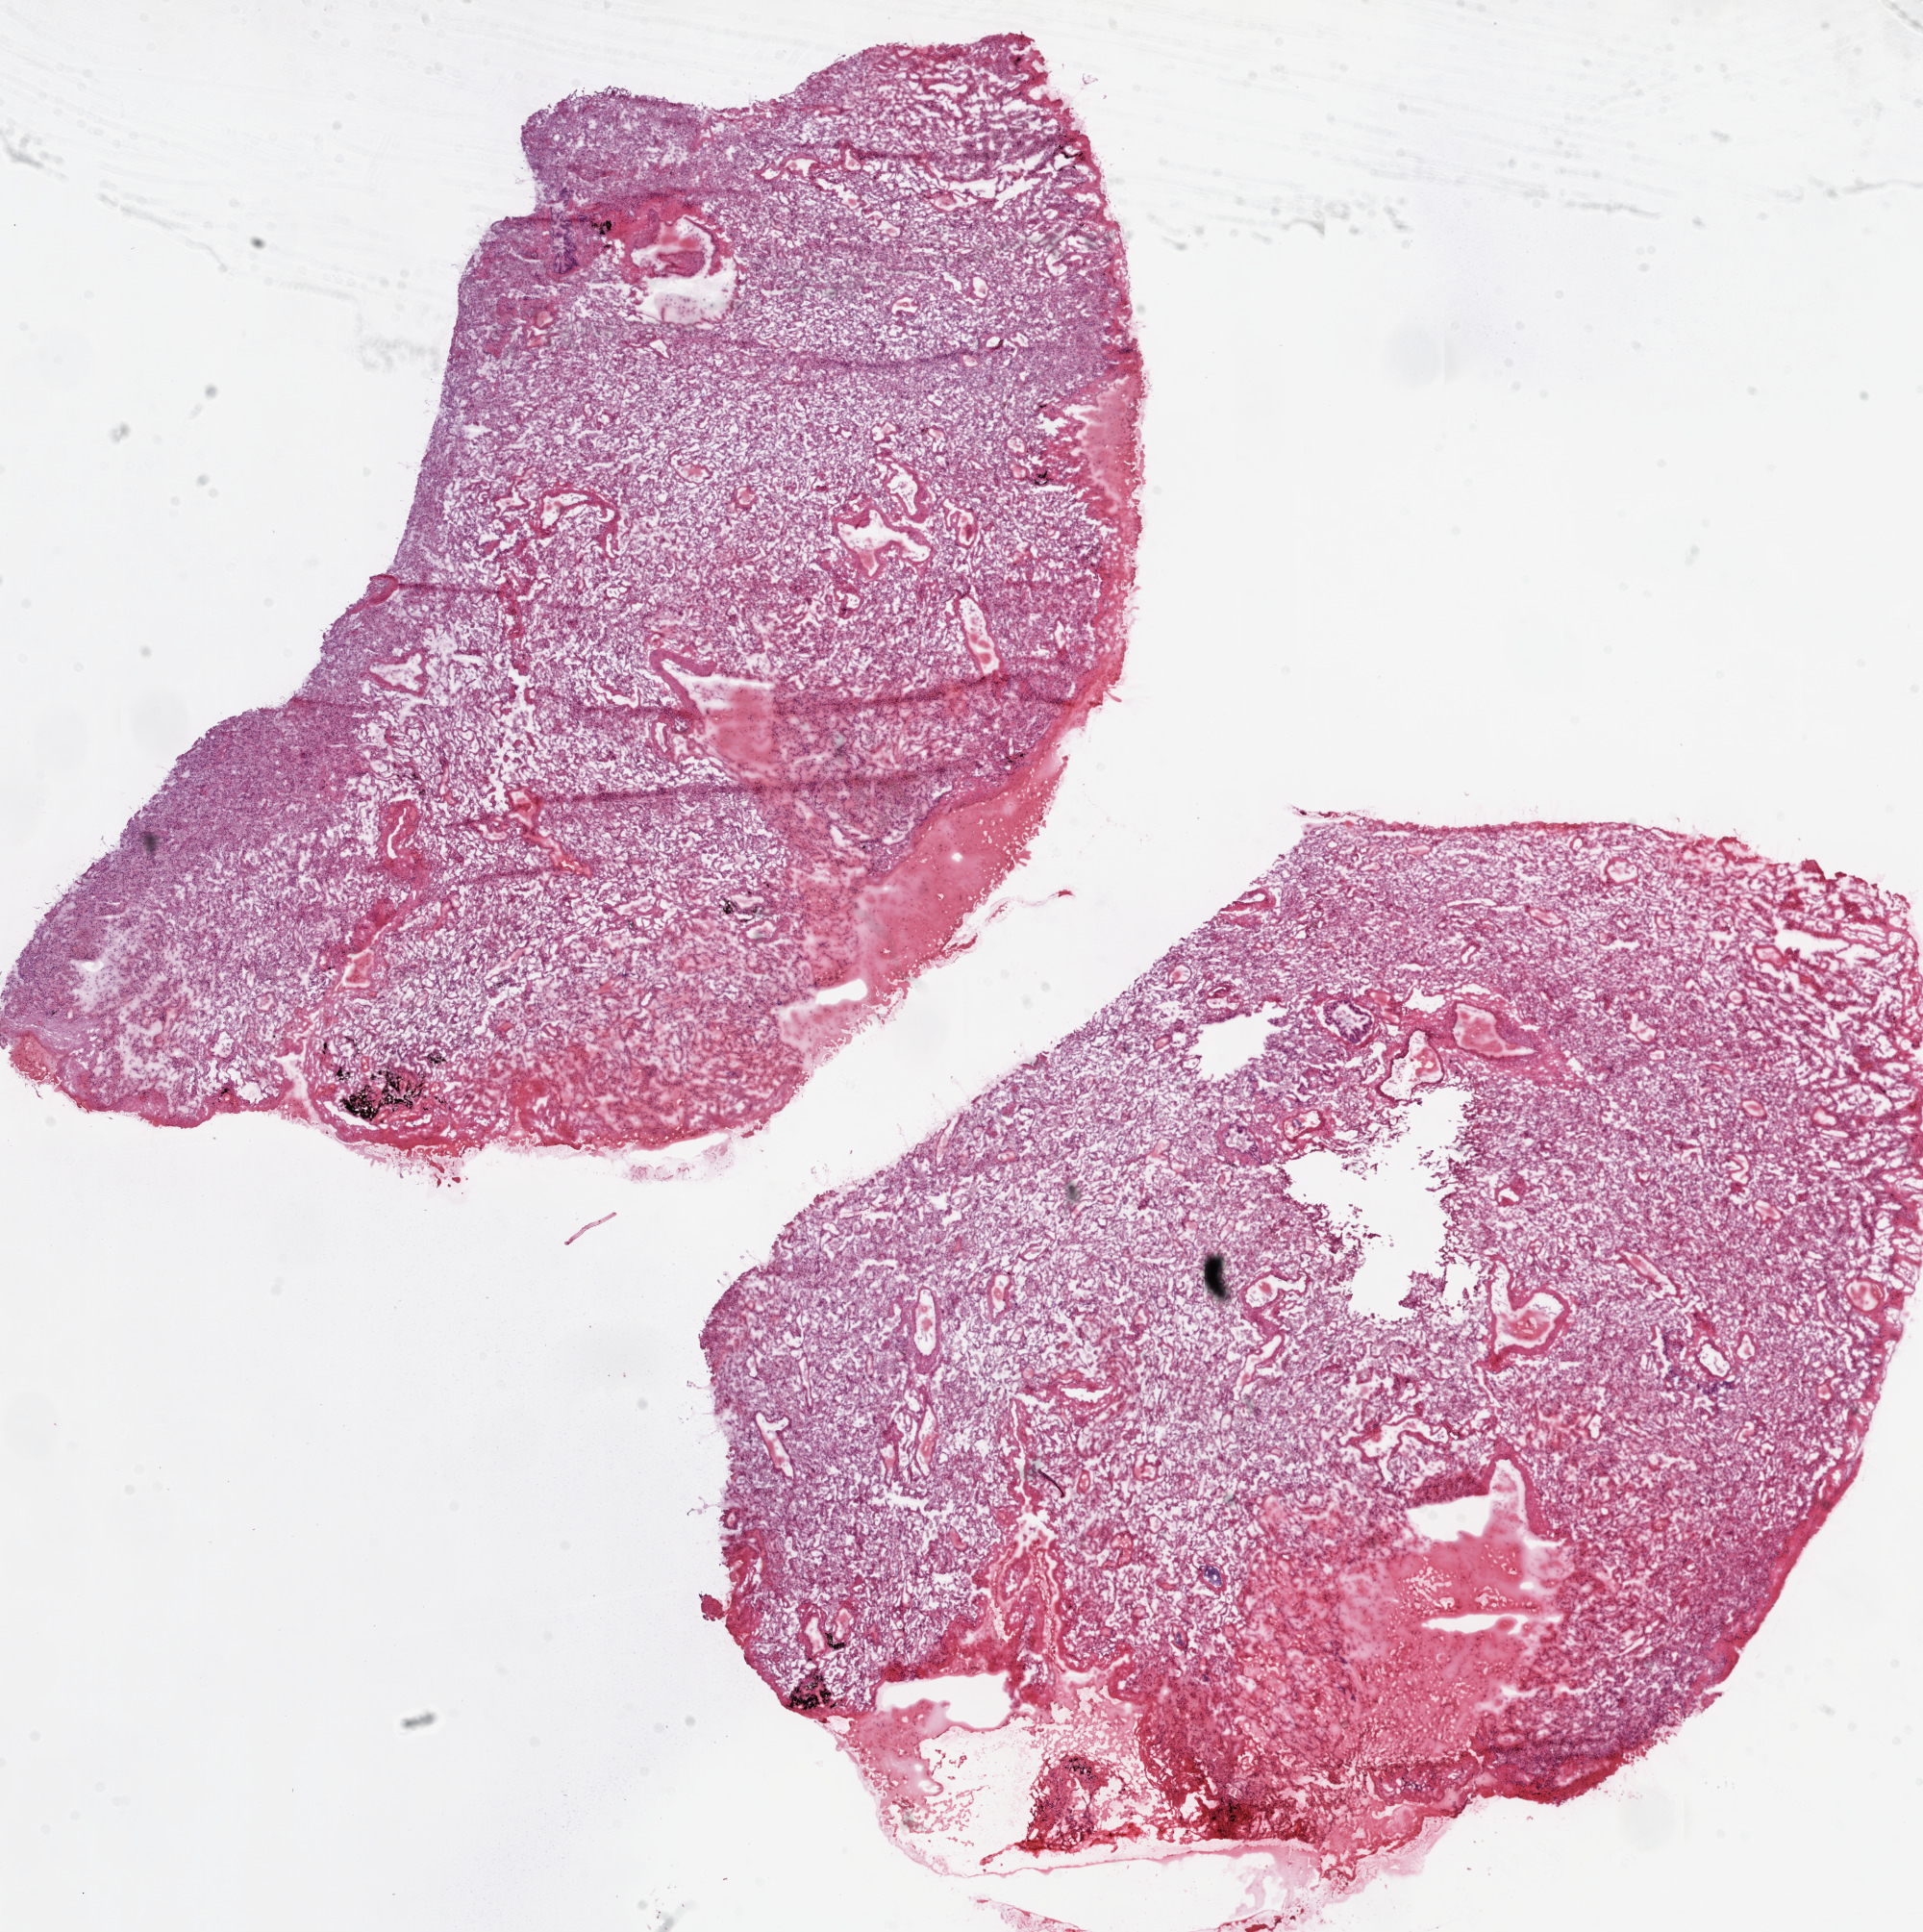
Whole-slide histology image, H&E-stained, shown as a low-resolution overview of the whole scanned area (about 16.0 x 16.1 mm, from a 20x scan). Frozen section from the top of the tissue portion. Lung, solid tissue normal (non-tumour tissue) sample. Male patient; age at initial diagnosis 40 years.
This section: solid tissue normal (non-tumour) sample from the same patient. Patient diagnosis: Squamous cell carcinoma, NOS (upper lobe, lung).